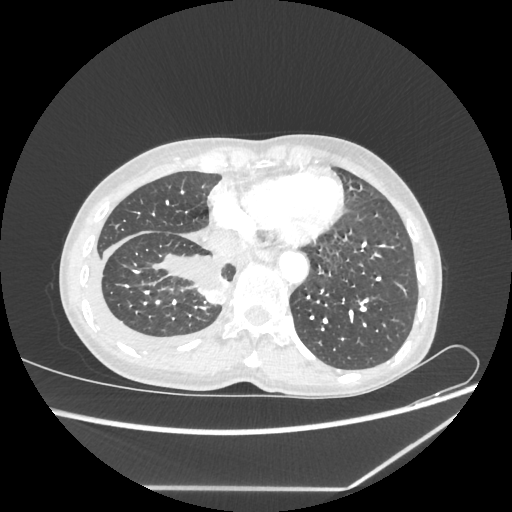
Chest CT, one axial slice. Position 61 of 237 along the scan axis. Lung window (W 1500 / L -600 HU). 1.25 mm slice thickness. 512 × 512 image matrix, field of view 364 × 364 mm. Female patient, age 59 years. From the clinical record (not read from this slice): clinical TNM (as recorded): T1c N1 M1.
Outlined on this slice (bounding box drawn by a radiologist):
- lung tumour (recorded histology: adenocarcinoma): box from (x=195, y=281) to (x=227, y=306) px